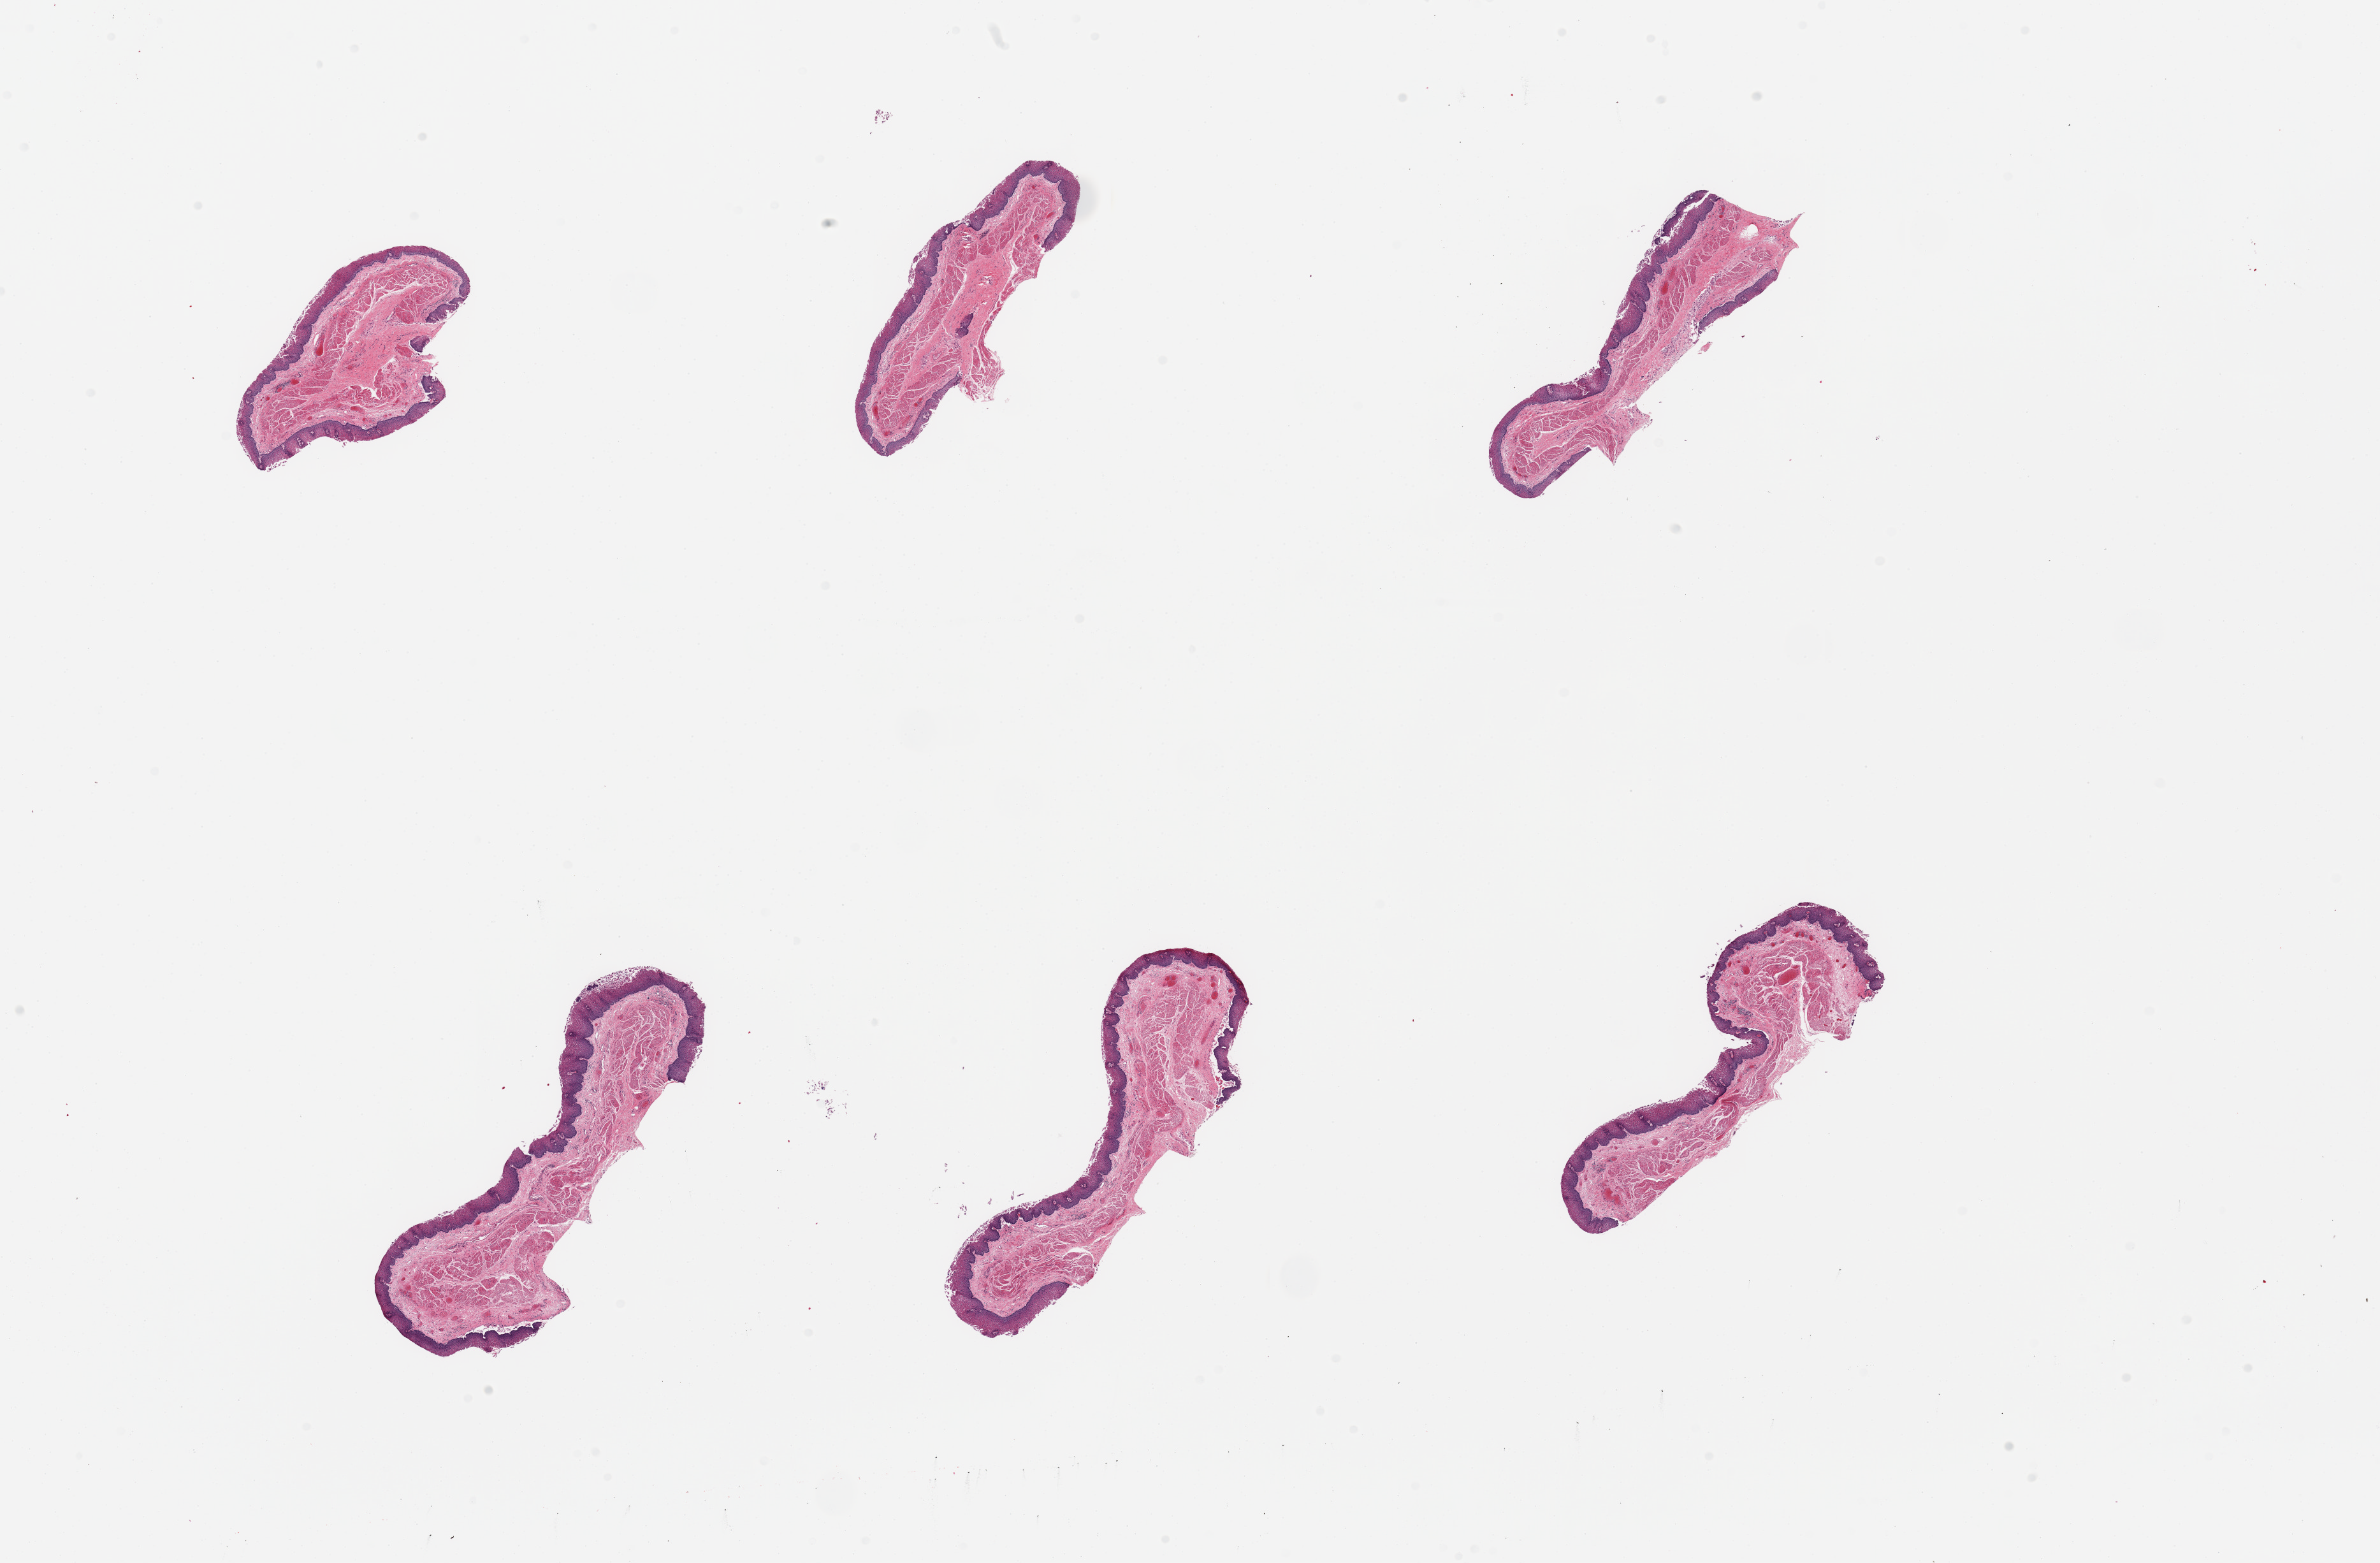
Digitized haematoxylin and eosin-stained section, brightfield, a low-resolution overview of the entire scanned area, about 29.5 x 19.4 mm. PAXgene-fixed, paraffin-embedded tissue. Target tissue: esophageal mucous membrane. Donor tissue sample.
Pathologist's review note for this sample: 6 pieces, squamous mucosa is ~10% thickness.